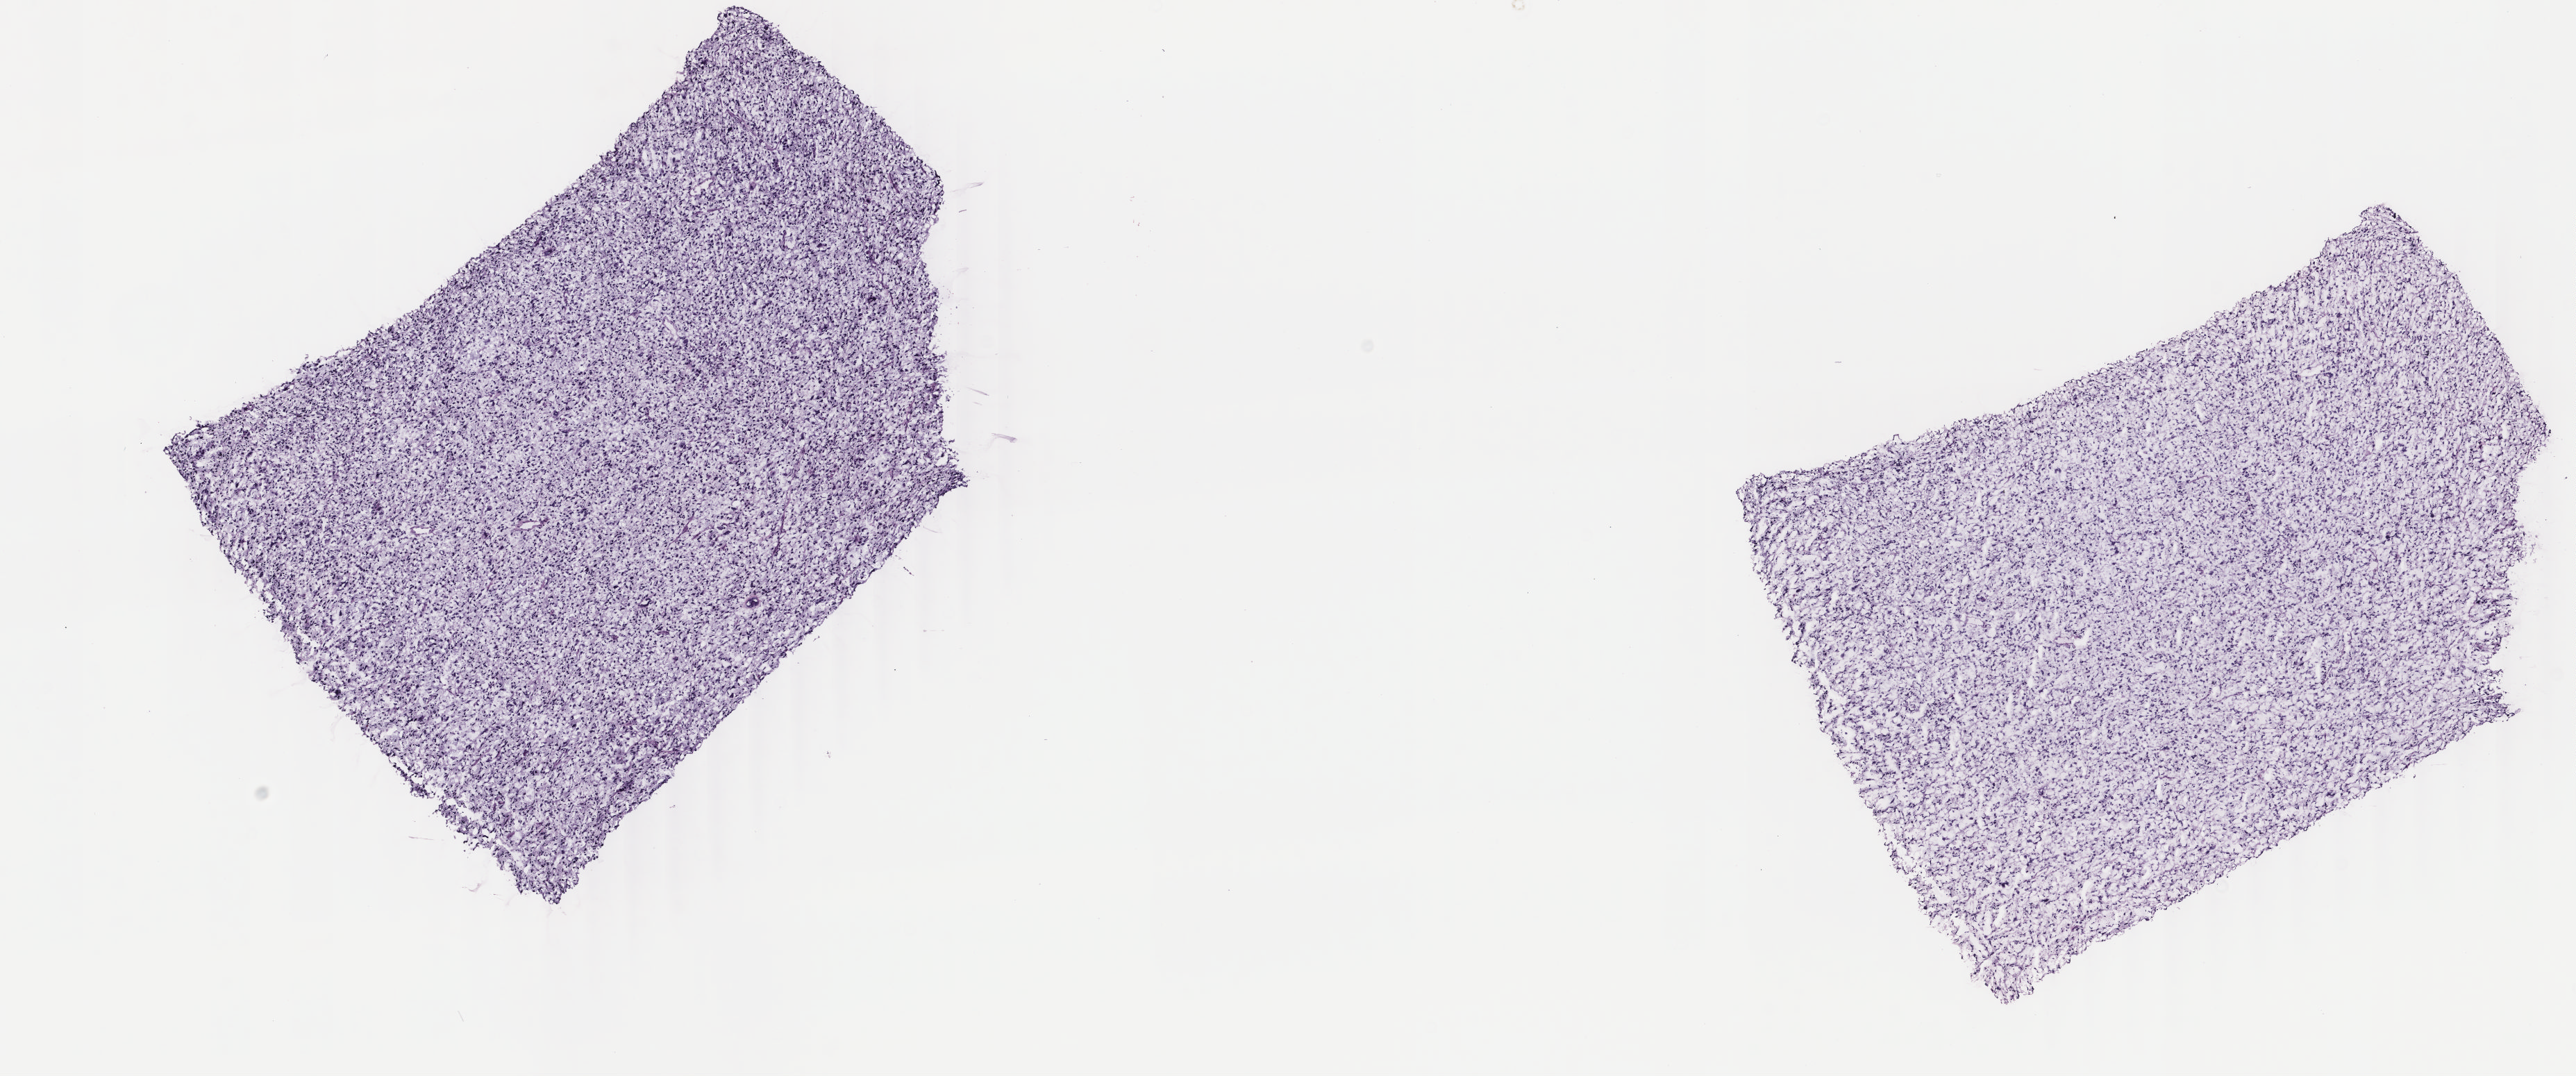
Digitized H&E-stained tissue section (whole slide) — whole scanned area (about 14.8 x 6.2 mm, from a 40x scan) shown as a low-resolution overview, frozen section from the top of the tissue portion, sample: primary tumour, retroperitoneum and peritoneum. Patient: female, age at initial diagnosis 55 years. Slide review estimates, as recorded: tumour cells 100%, tumour nuclei 94%, normal cells 0%, stromal cells 0%, necrosis 0%. Inflammatory infiltration, as recorded: lymphocyte infiltration 0%, monocyte infiltration 0%, neutrophil infiltration 0%.
Histologic diagnosis: Dedifferentiated liposarcoma (retroperitoneum).